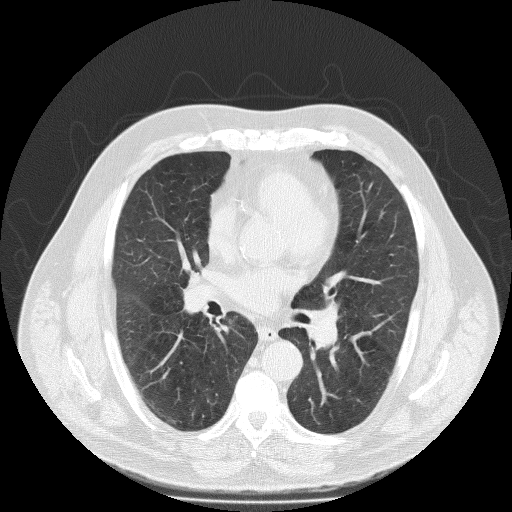
Low-dose screening chest CT, axial slice. Baseline screening round. Lung window (W 1500 / L -600 HU). 2 mm slice thickness. Lung (sharp) reconstruction kernel (FC51). Slice 100 of 204 in the series. Male participant, aged 65 years at enrolment.
- Lesion marked by an expert reader, box from (x=205, y=306) to (x=249, y=334) px.
- The screening reader recorded 2 non-calcified nodules or masses ≥4 mm on this exam (right lower lobe, right middle lobe); which of them this box marks is not recorded.
- Official screen result: positive, change unspecified: nodule(s) >= 4 mm or enlarging nodule(s), mass(es), or other non-specific abnormalities suspicious for lung cancer.
- Participant outcome: lung cancer diagnosed 651 days after this screen — large cell neuroendocrine carcinoma, right lower lobe, undifferentiated (G4), stage IIIA (AJCC 6th edition).